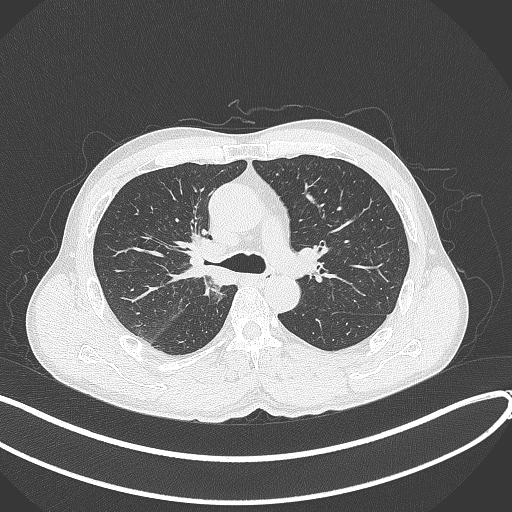
Chest CT, one axial slice. Position 251 of 409 along the scan axis. Lung window (W 1500 / L -600 HU). 1 mm slice thickness. 512 × 512 image matrix. Male patient, age 53 years. Case-level facts recorded for this patient, not image findings: clinical TNM (as recorded): T1b N0 M0.
Outlined on this slice (bounding box drawn by a radiologist):
- lung tumour (recorded histology: squamous cell carcinoma): bounding box (x1, y1, x2, y2) in pixels: (179, 228, 231, 283)